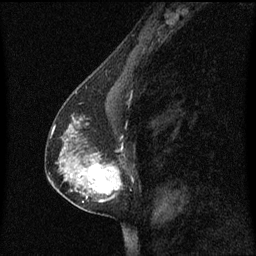
Breast MRI (dynamic contrast-enhanced), one sagittal slice. Slice 34 of 60 in the series (ordered by position). Dynamic contrast-enhanced series, image 2 of 3 at this slice position (ordered by acquisition). 1.5 T. TE 4.2 ms, TR 8.4 ms. 2 mm slice thickness. 256 × 256 image matrix, field of view 200 × 200 mm. Patient: female, 40 years. From the clinical record (not read from this slice): setting: breast cancer imaged before/during neoadjuvant chemotherapy; receptor status: triple-negative.
Annotated regions visible in this slice (semi-automatic segmentation, software-assisted and operator-edited):
- analysis volume of interest (the breast-tissue region the enhancement analysis was run in; not a lesion): box from (x=60, y=104) to (x=131, y=213) px
- tumour enhancement mask (voxels above the 70 % enhancement threshold inside the analysis volume of interest): (x=72, y=130)–(x=121, y=203)